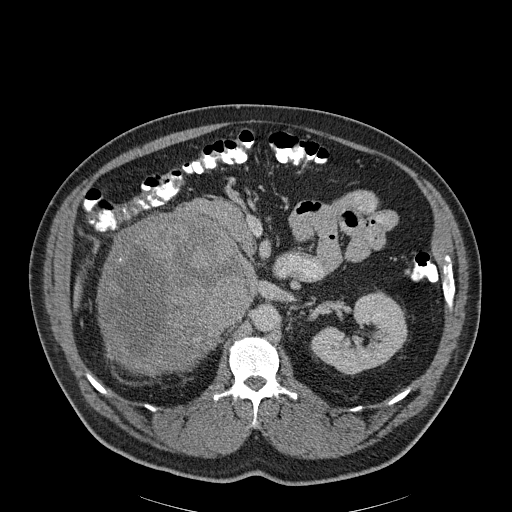
Contrast-enhanced abdominal CT, one axial slice; position 121 of 186 along the scan axis; reconstruction kernel B30f; 120 kVp; soft-tissue window (W 400 / L 40 HU); 3 mm slice thickness; 512 × 512 image matrix, field of view 464 × 464 mm. Patient: male, 56 years. Case-level facts recorded for this patient, not image findings: diagnosis: adrenocortical carcinoma; tumour side: right adrenal; tumour size at pathology: 18 cm; Ki-67 index: 2 %; stage (as recorded): 3.
Structures marked on this image (semi-automatic segmentation, software-assisted and operator-edited):
- mass: bounding box (x1, y1, x2, y2) in pixels: (101, 213, 247, 373)